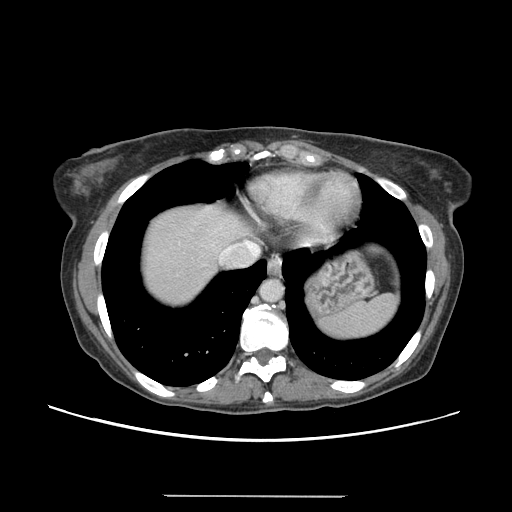
Contrast-enhanced abdominal CT, one axial slice; position 130 of 144 along the scan axis; 120 kVp; soft-tissue window (W 400 / L 40 HU); 512 × 512 image matrix, field of view 380 × 380 mm. Female patient, age 53 years. Case-level facts recorded for this patient, not image findings: diagnosis: colorectal cancer liver metastases, imaged before liver resection; multiple liver metastases: yes; largest metastasis: 1.1 cm; disease in both lobes: no.
Outlined on this slice (expert manual segmentation):
- hepatic veins: bounding box <220,241,260,260> (left, top, right, bottom; pixels)
- liver: <139,205,246,306>
- planned liver remnant (the part of the liver to remain after resection): <140,202,247,289>